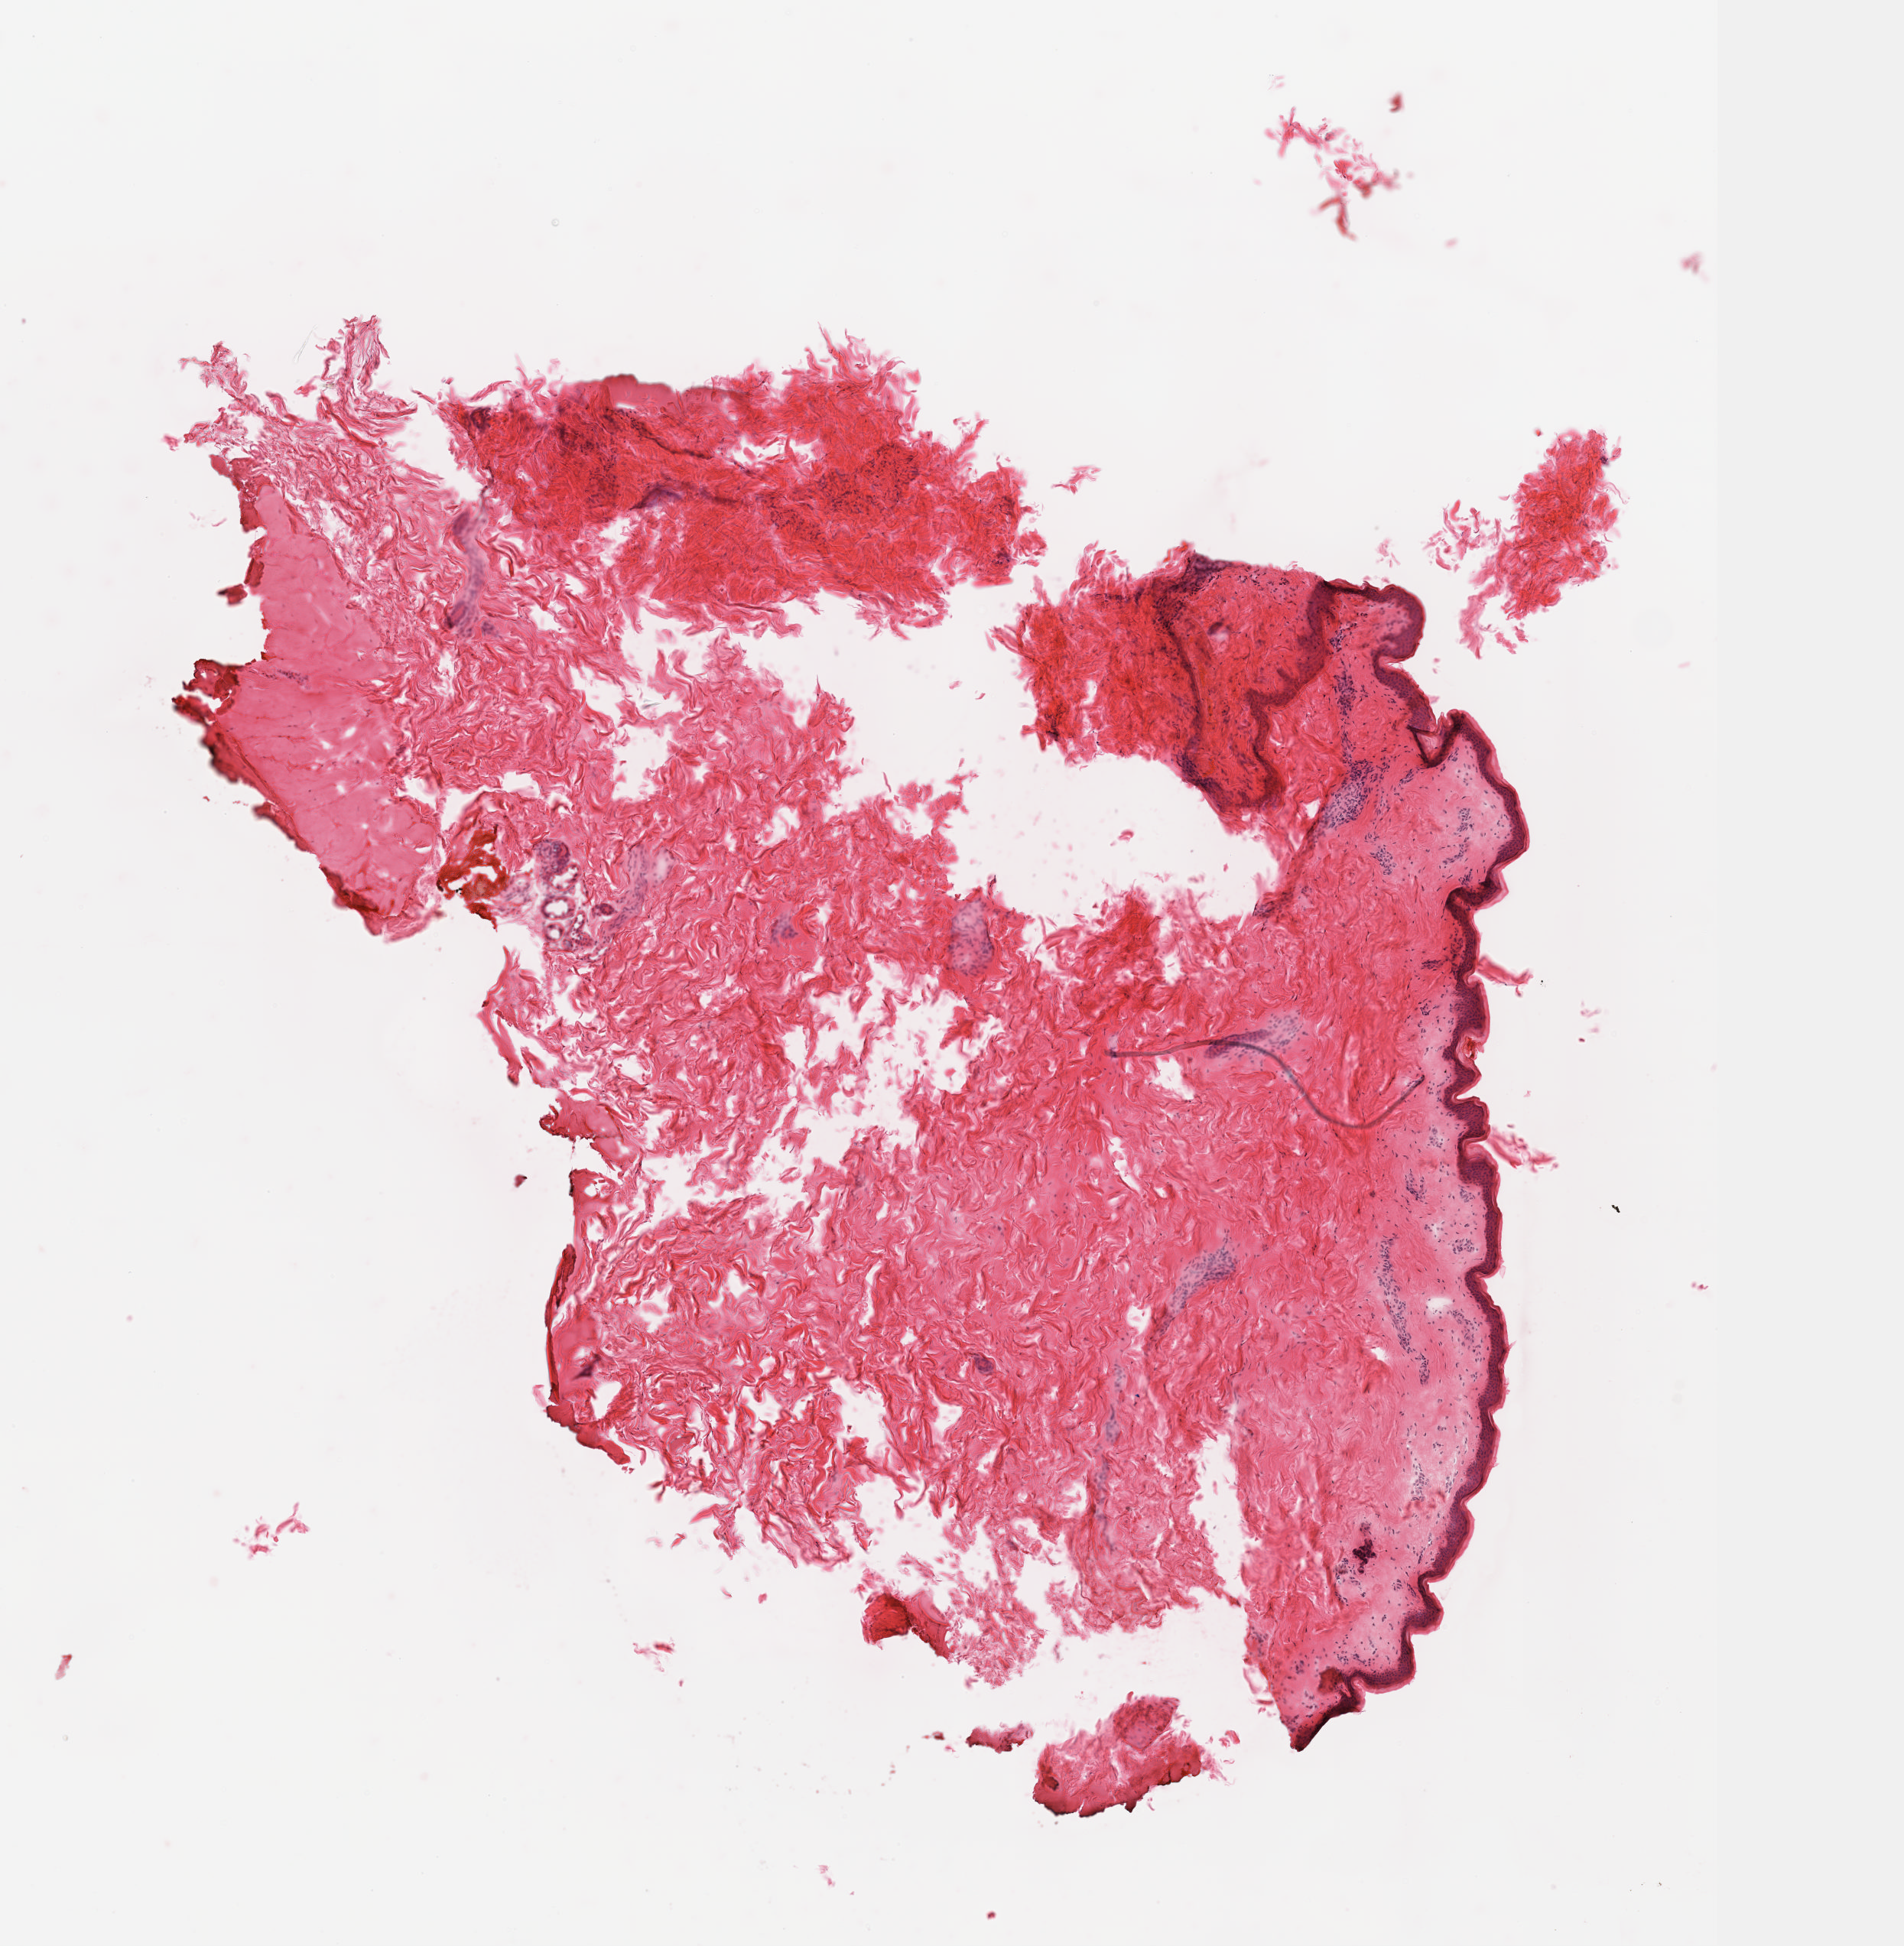
H&E whole-slide image, low-resolution overview of the scanned area, about 5.0 x 5.1 mm (acquisition: 40x scan); frozen section; solid tissue normal (non-tumour tissue) sample from the cervix. Female, age 44 years at initial diagnosis. Composition of this section per pathologist review: tumour cells 0%, tumour nuclei 0%, normal cells 100%, stromal cells 0%, necrosis 0%. Inflammatory infiltration, as recorded: lymphocyte infiltration 0%, monocyte infiltration 0%, neutrophil infiltration 0%.
This section: solid tissue normal sample (biorepository sample class). Patient diagnosis: Squamous cell carcinoma, NOS (cervix uteri).